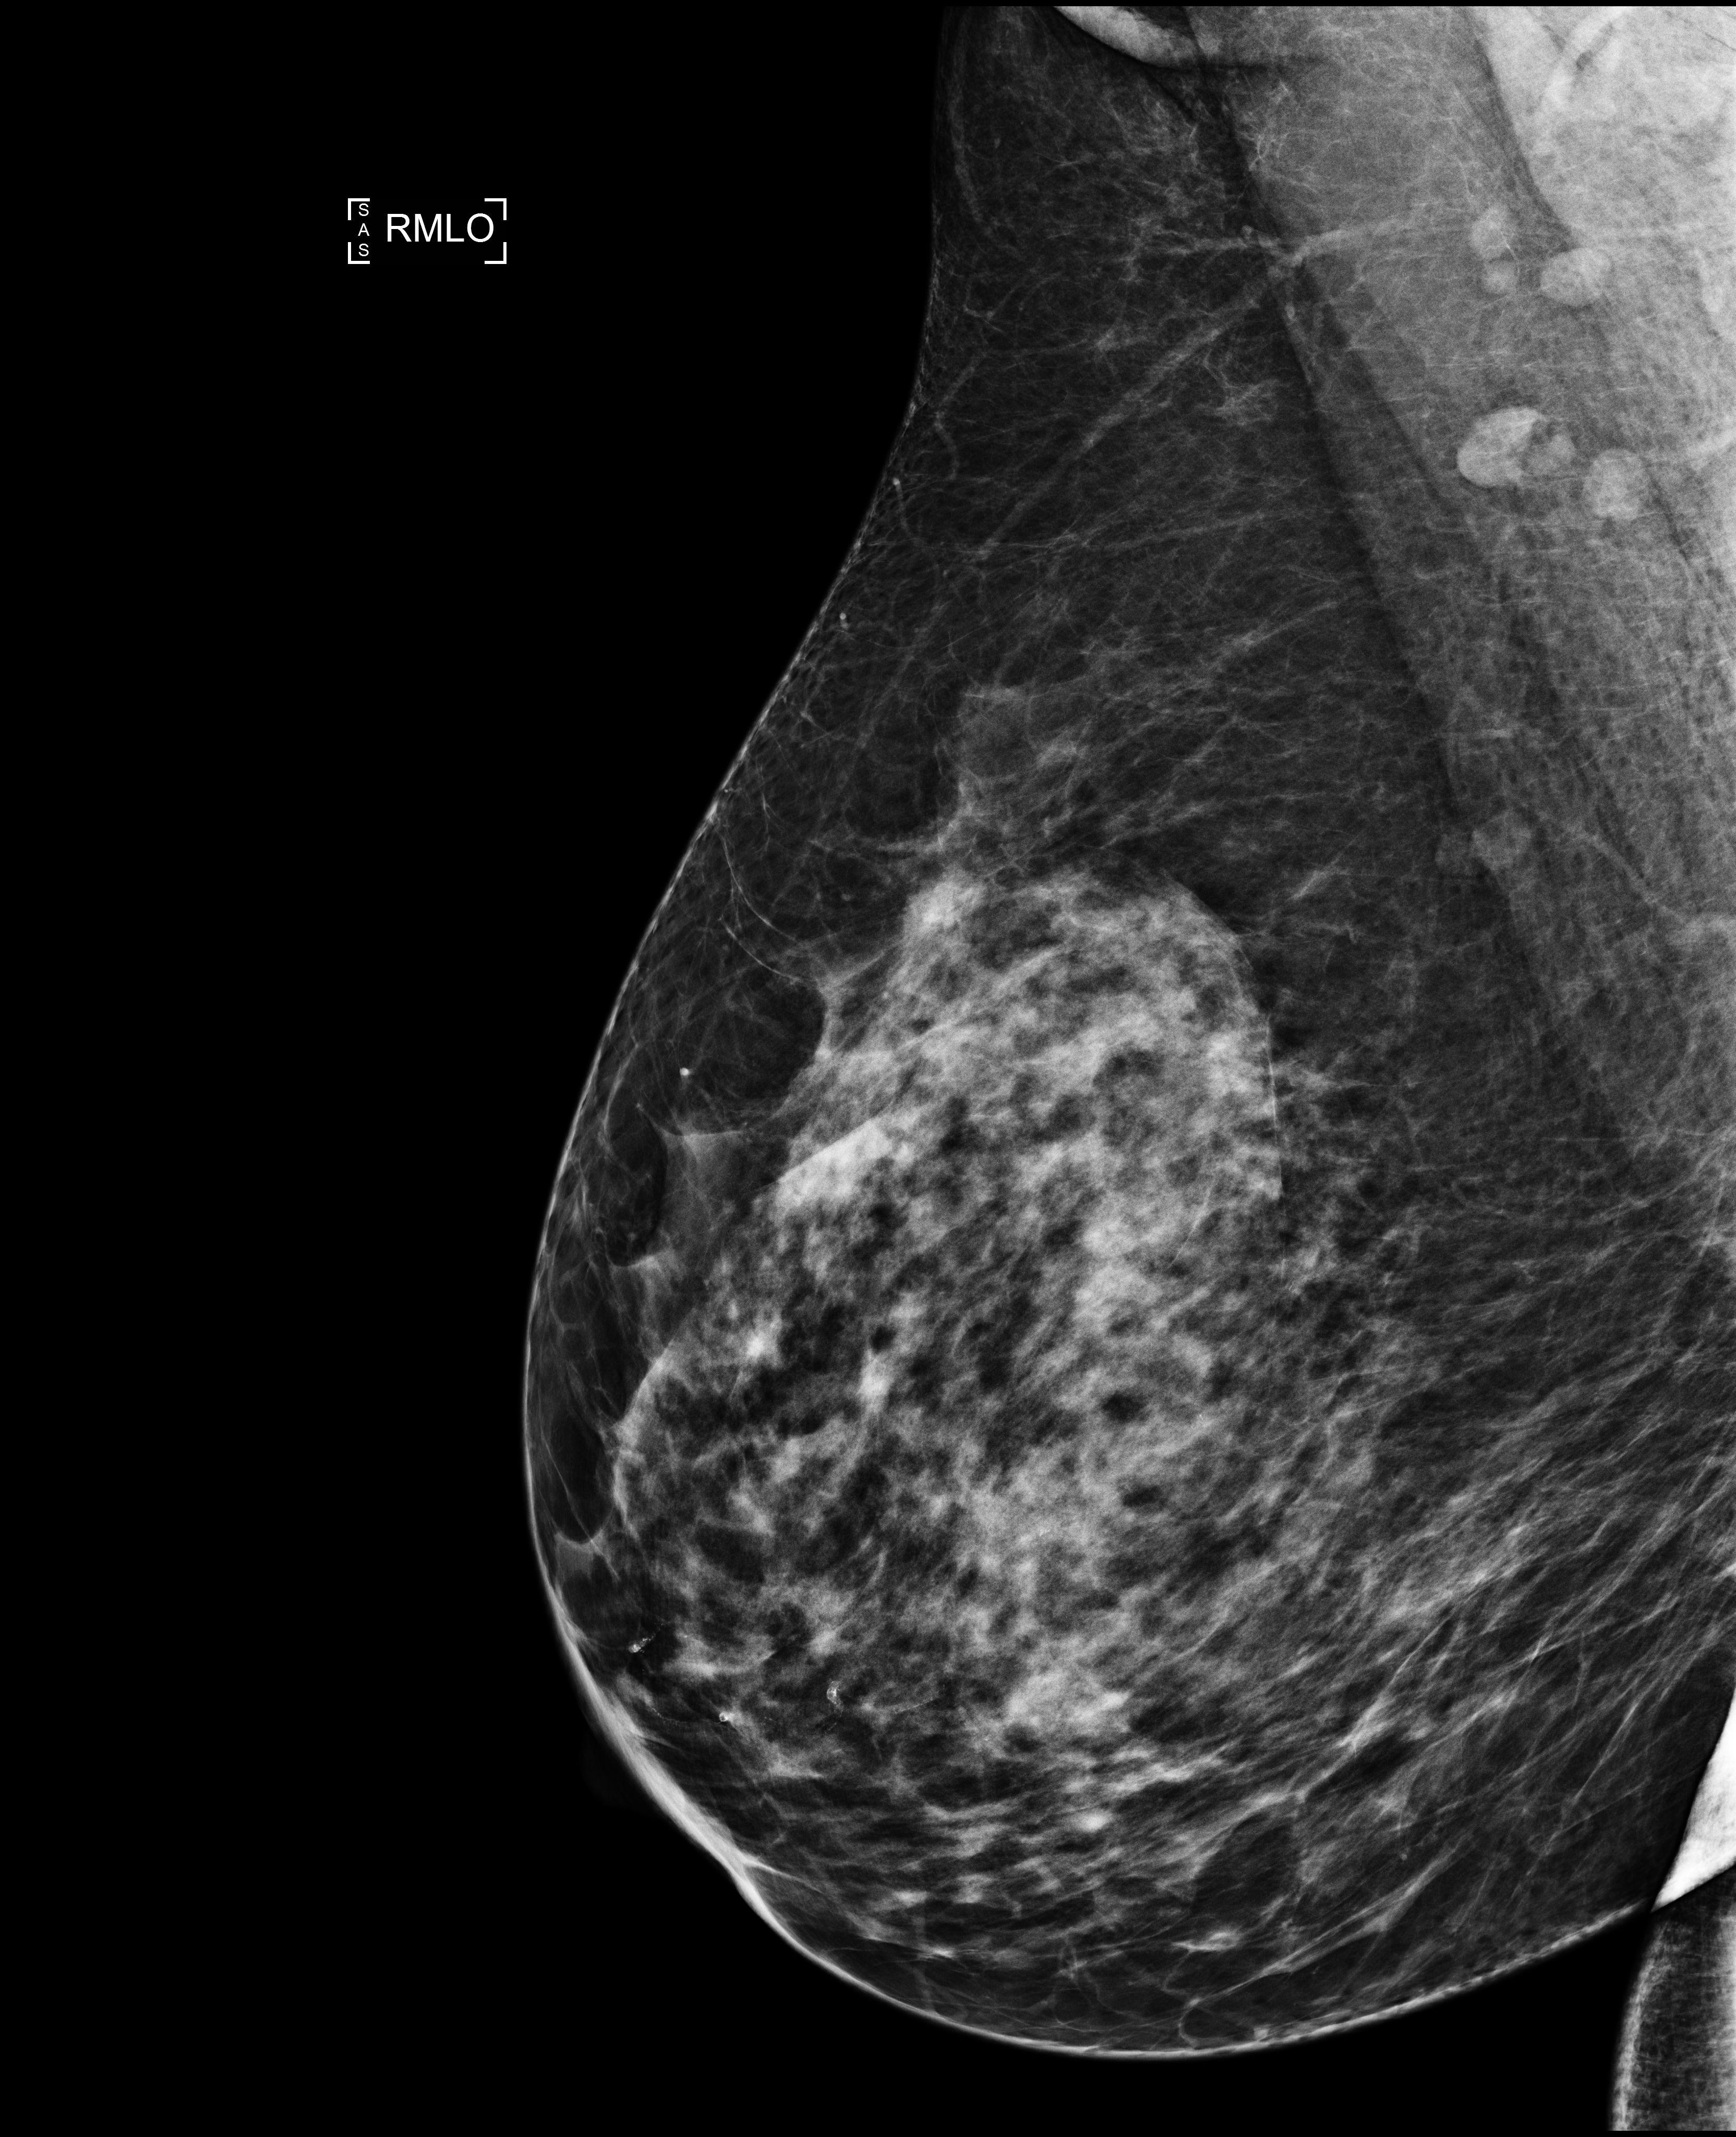
Screening examination. Female patient, age 44 years.
Image type: full-field digital mammogram. Breast: right. Projection: medio-lateral oblique projection.